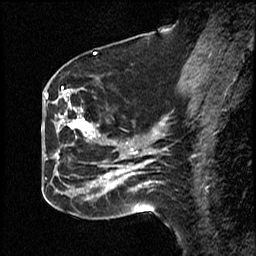
Breast MRI (dynamic contrast-enhanced), one sagittal slice; slice 24 of 50 in the series (ordered by position); dynamic contrast-enhanced study with each time point stored as its own series, time point 2 of 4 at this slice position (early post-contrast, ordered by acquisition time); 1.5 T; TE 4.2 ms, TR 18.5 ms; 256 × 256 image matrix, field of view 200 × 200 mm. Patient: female, 44 years. Case-level facts recorded for this patient, not image findings: setting: breast cancer imaged before/during neoadjuvant chemotherapy; receptor status: HR-positive, HER2-negative.
Outlined on this slice (semi-automatic segmentation, software-assisted and operator-edited):
- analysis volume of interest (the breast-tissue region the enhancement analysis was run in; not a lesion): bounding box [x1, y1, x2, y2] px = [59, 88, 114, 201]
- tumour enhancement mask (voxels above the 100 % enhancement threshold inside the analysis volume of interest): [63, 91, 114, 188]